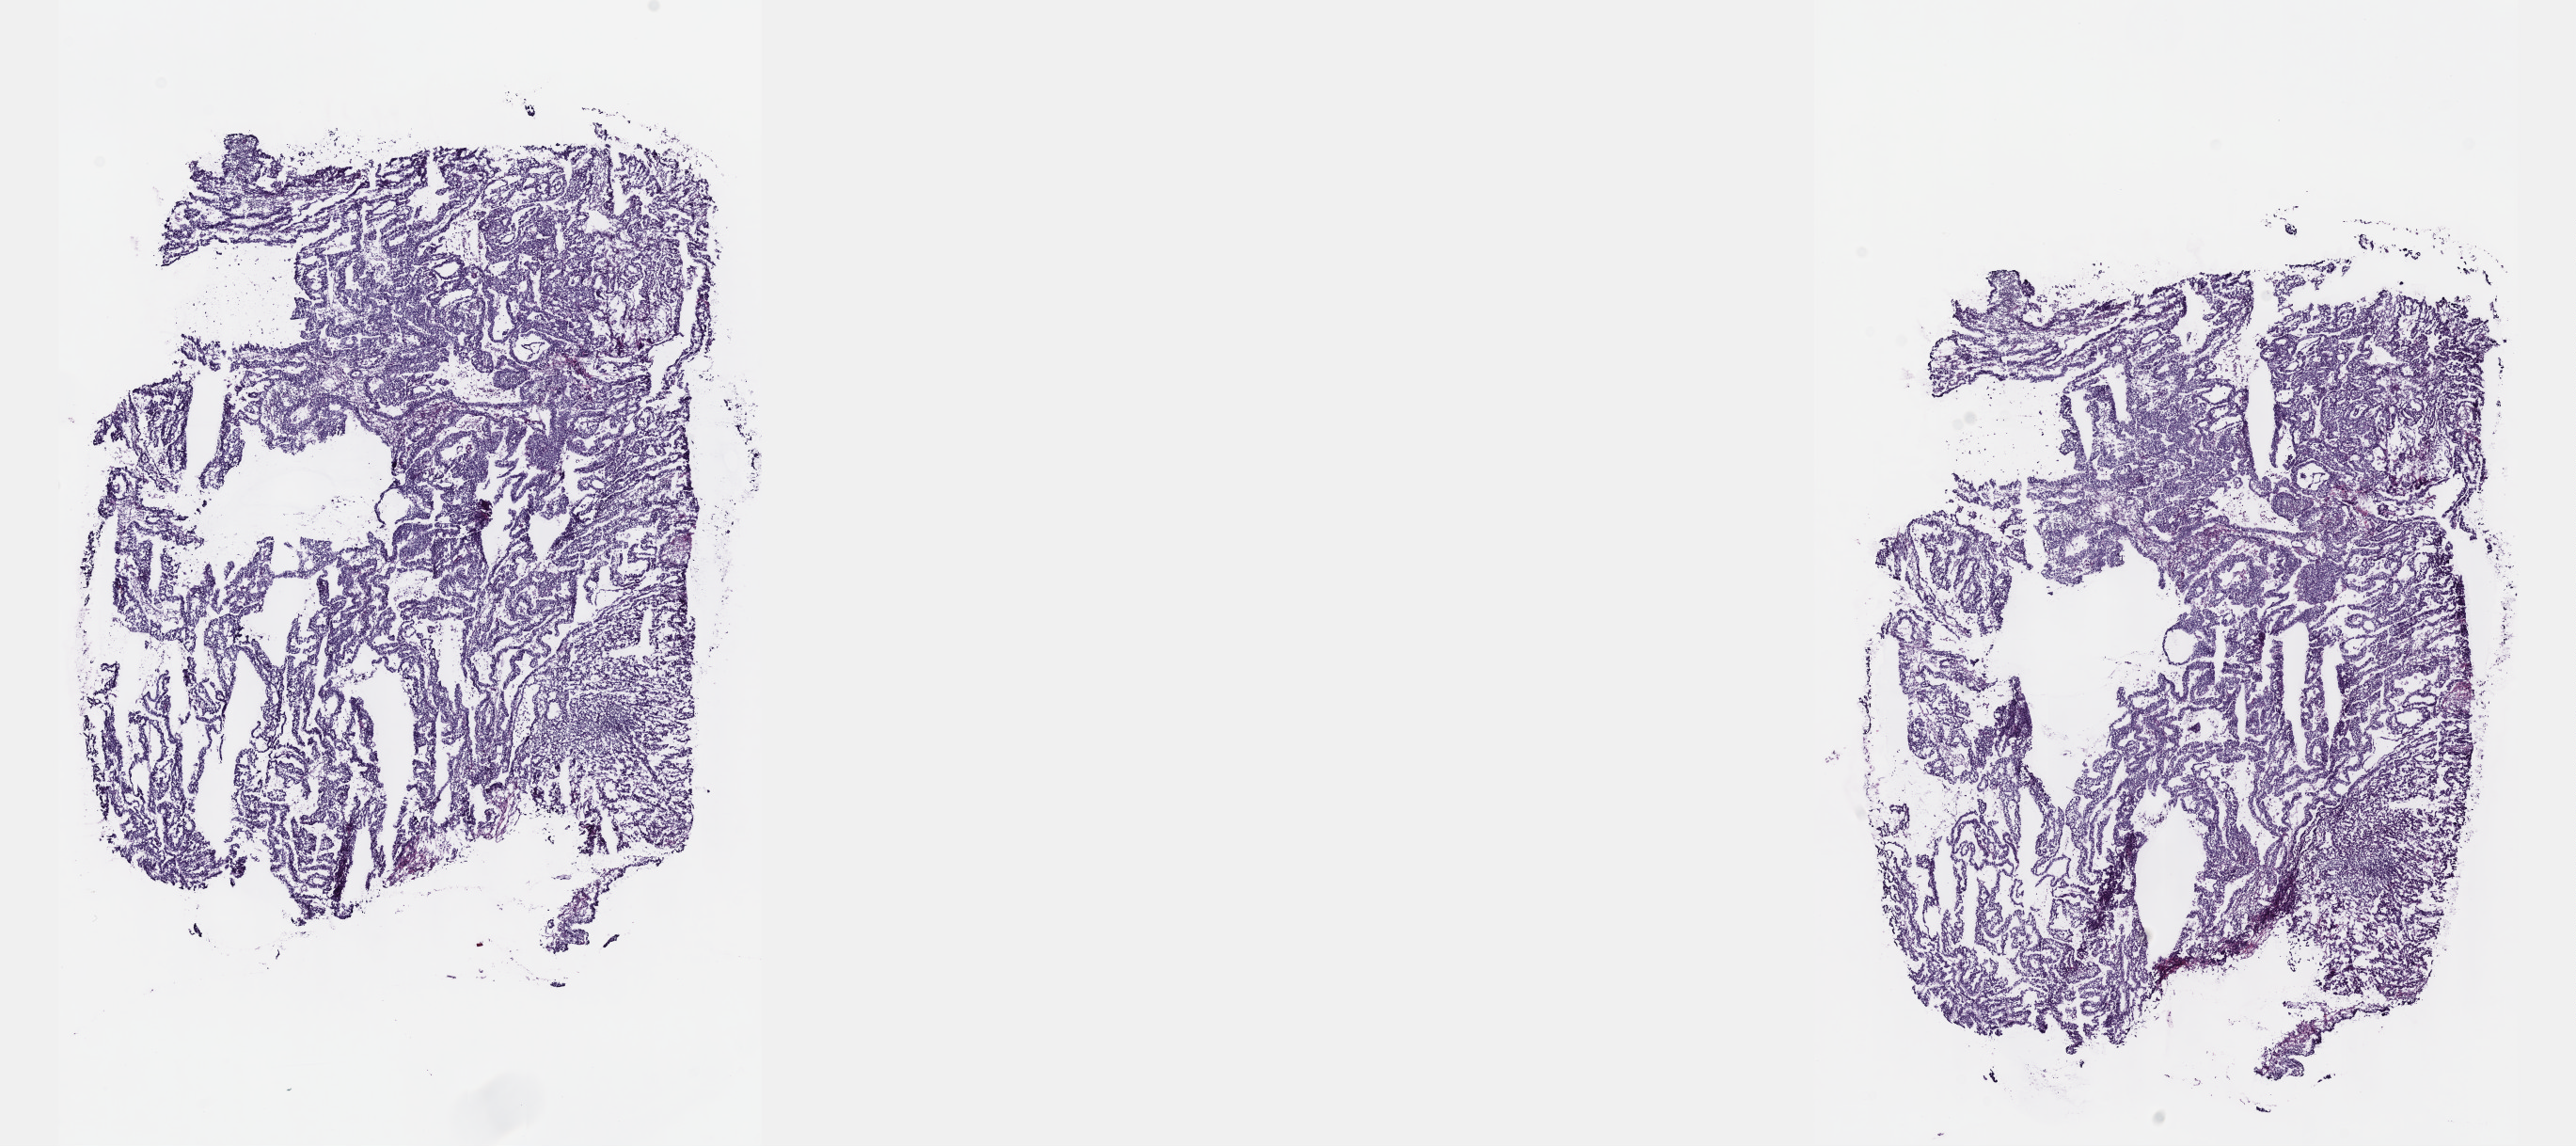
Hematoxylin and eosin (H&E) stained whole-slide image — shown as a low-resolution overview of the whole scanned area (about 22.1 x 9.8 mm). Patient sex: male. Composition of this section per pathologist review: tumour cells 100%, tumour nuclei 75%, normal cells 0%, stromal cells 0%, necrosis 0%. Infiltration values recorded for this section: lymphocyte infiltration 3%, monocyte infiltration 0%, neutrophil infiltration 0%.
• specimen: frozen section from the top of the tissue portion; primary tumour sample from the testis